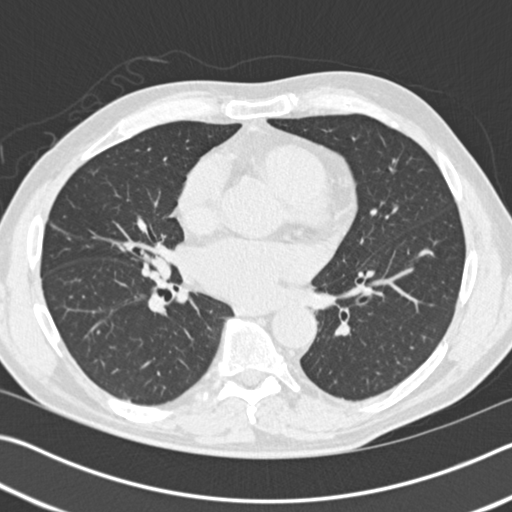
Axial slice from a low-dose chest CT screening exam. Baseline screening round. Lung window (W 1500 / L -600 HU). 120 kVp. 512 × 512 image matrix, field of view 340 × 340 mm. Male participant, aged 57 years at enrolment.
Expert reader's lesion annotation, box from (x=142, y=247) to (x=179, y=284) px. The screening reader recorded 2 non-calcified nodules or masses ≥4 mm on this exam; which of them this box marks is not recorded.